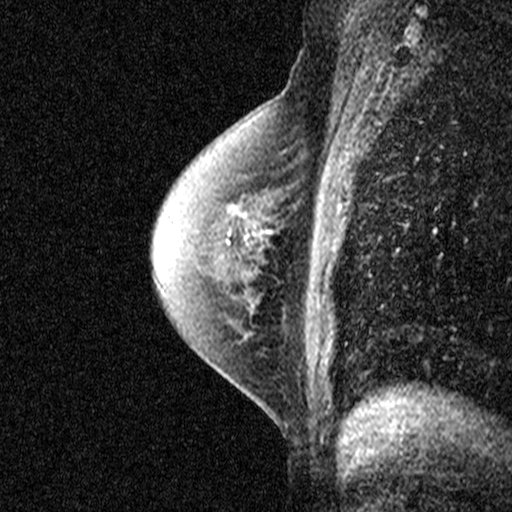
Breast MRI (dynamic contrast-enhanced), one sagittal slice. Dynamic contrast-enhanced study with each time point stored as its own series, time point 2 of 3 at this slice position (early post-contrast, ordered by acquisition time). 1.5 T. TE 4.5 ms, TR 11 ms. 3 mm slice thickness. 512 × 512 image matrix, field of view 200 × 200 mm. Patient: female, 55 years. Case-level facts recorded for this patient, not image findings: setting: breast cancer imaged before/during neoadjuvant chemotherapy; receptor status: HR-positive, HER2-negative.
Structures marked on this image (semi-automatic segmentation, software-assisted and operator-edited):
- analysis volume of interest (the breast-tissue region the enhancement analysis was run in; not a lesion): box from (x=194, y=202) to (x=279, y=277) px
- tumour enhancement mask (voxels above the 90 % enhancement threshold inside the analysis volume of interest): (x=244, y=236)–(x=247, y=240)